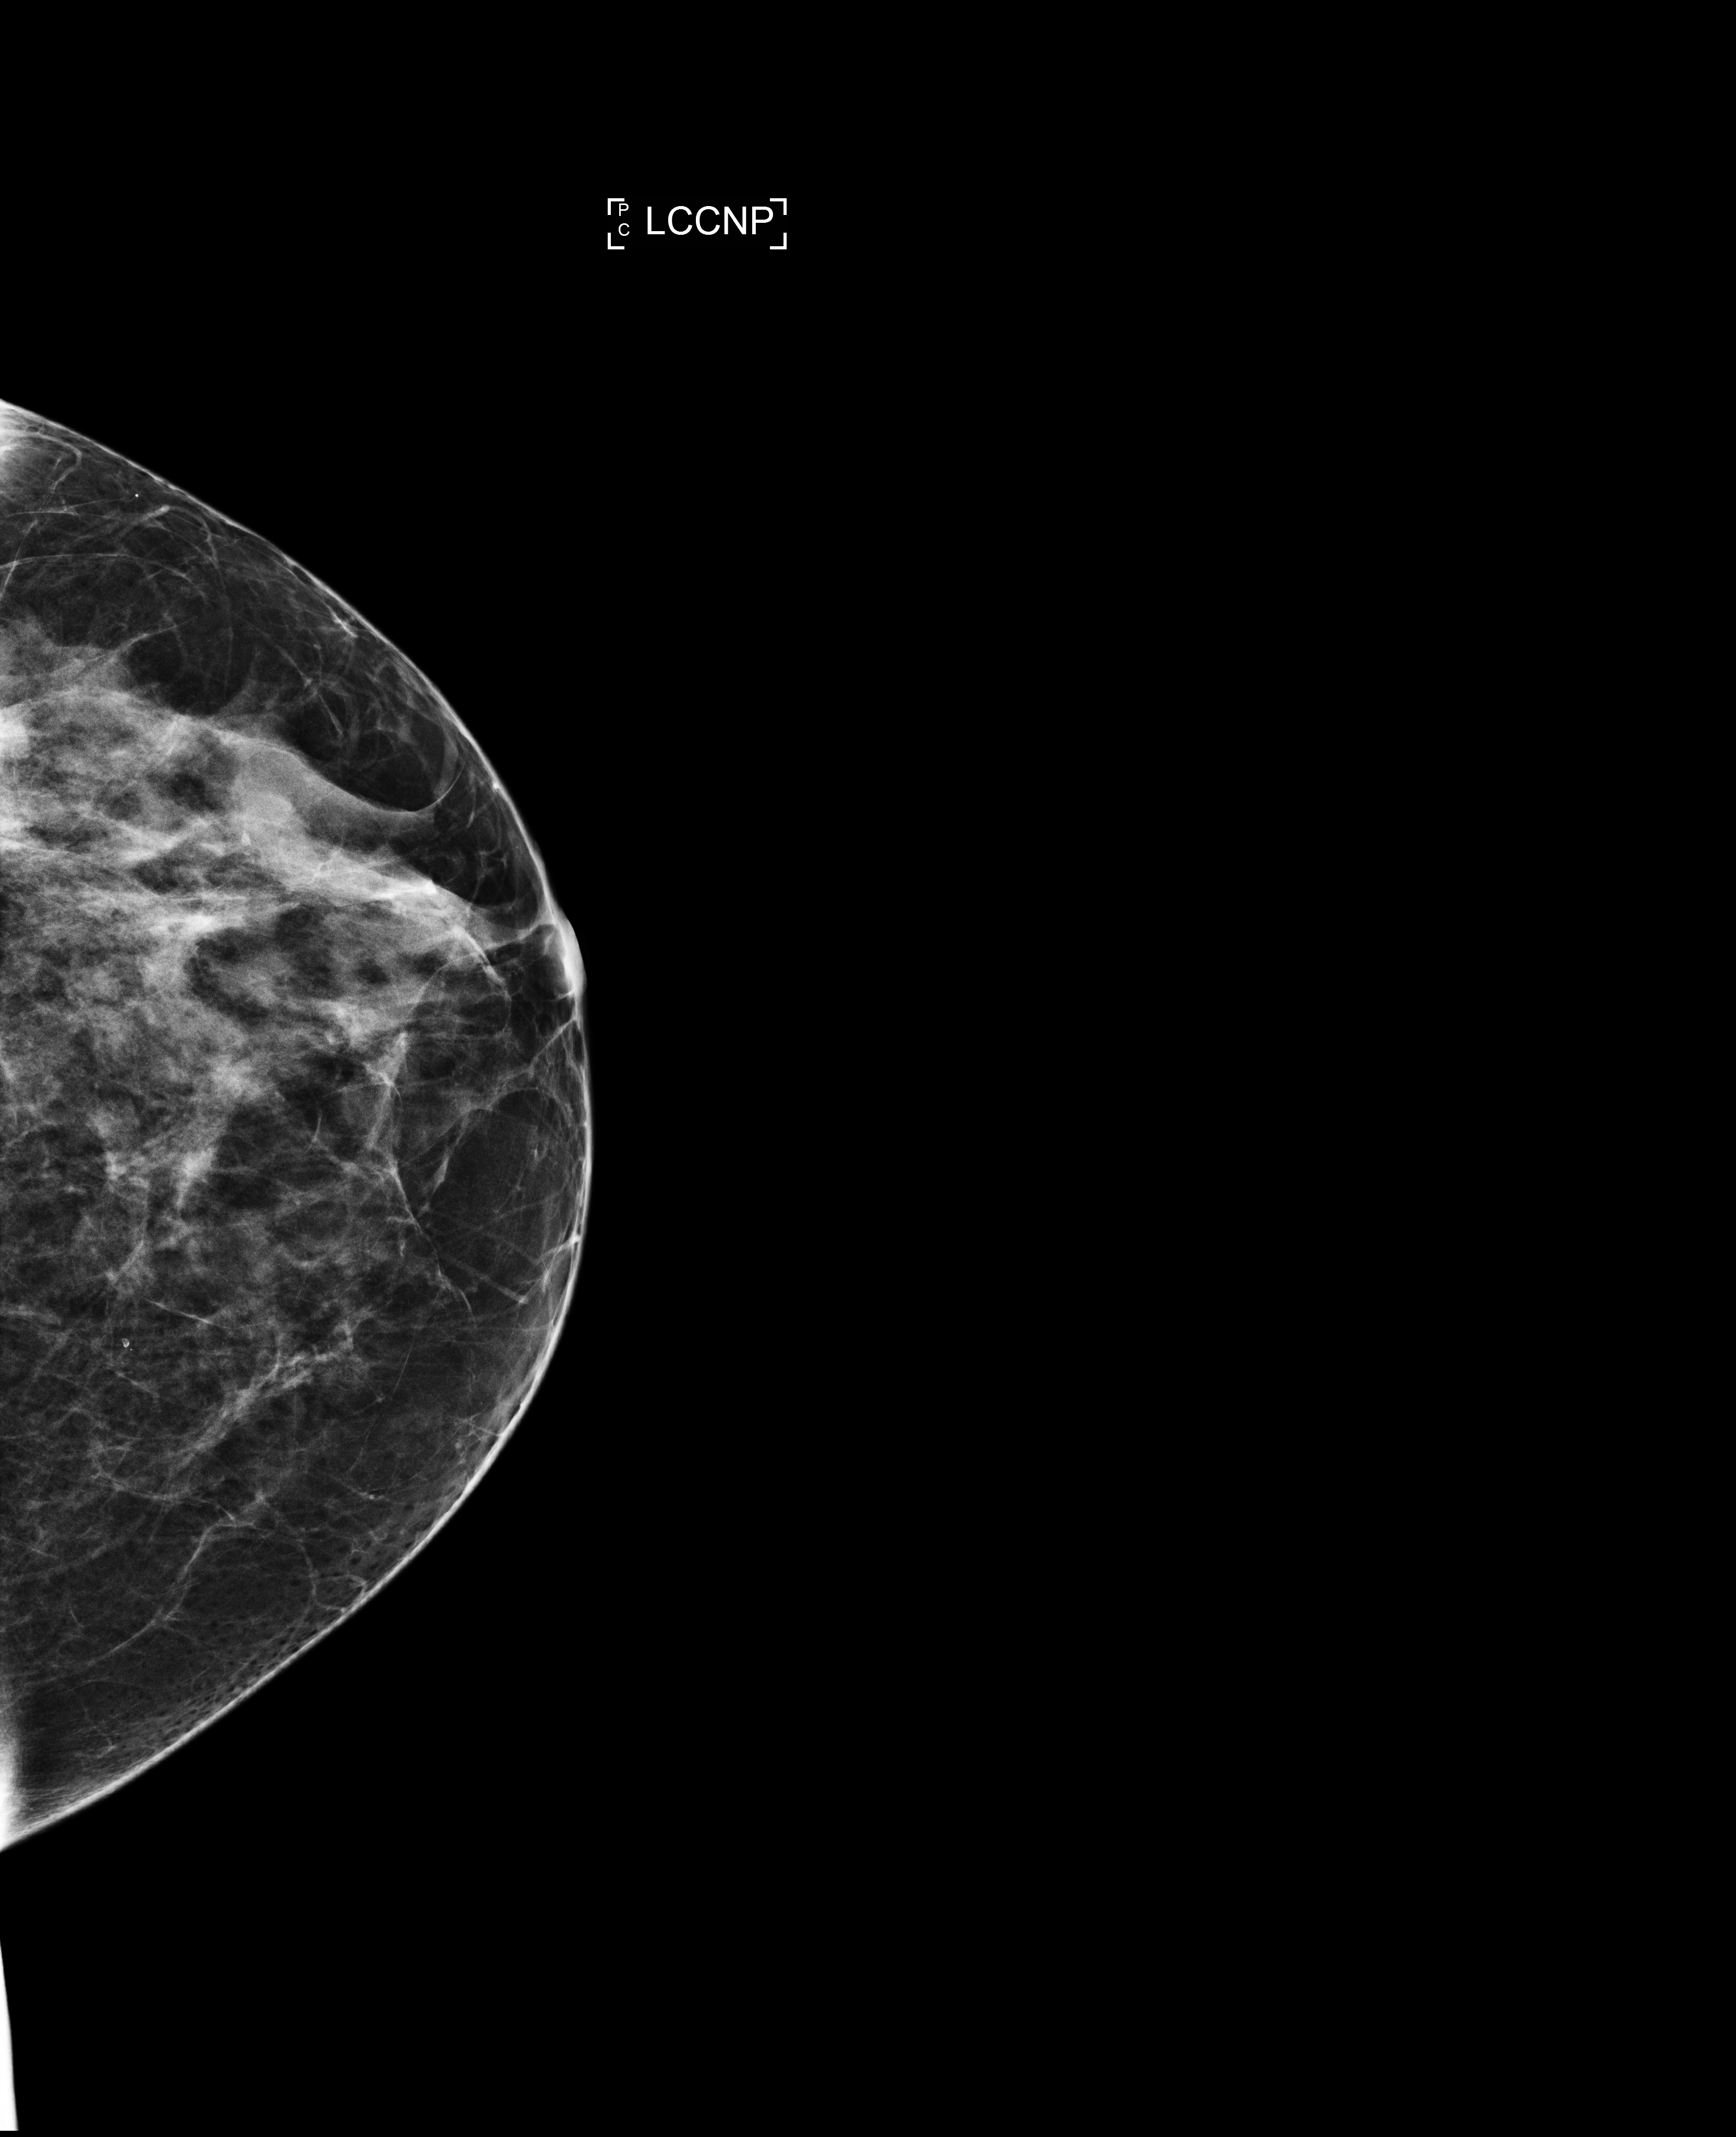
Annual screening mammography examination; compressed breast thickness 48 mm; system: Selenia Dimensions. Patient aged 49 years (female).
Image type: full-field digital mammogram. Breast: left. Projection: CC view, nipple in profile.